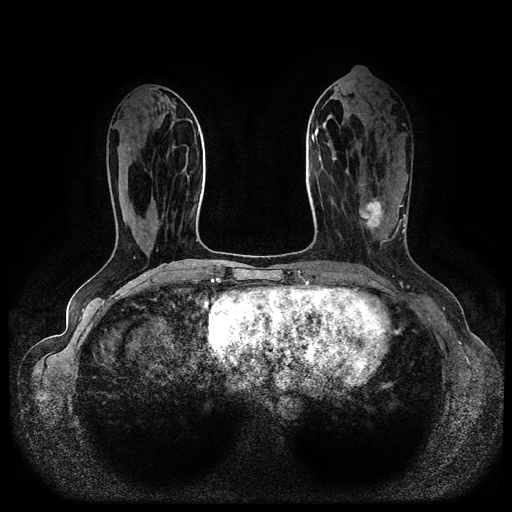
Breast MRI (dynamic contrast-enhanced, multi-phase), one axial slice; slice 38 of 116 in the series (ordered by position); dynamic contrast-enhanced series, time point 2 of 5 at this slice position (early post-contrast); 1.5 T; TE 2.6 ms, TR 5.3 ms; 2 mm slice thickness; 512 × 512 image matrix. Patient: female, 45 years.
Annotated regions visible in this slice (semi-automatically segmented with operator editing):
- breast lesion (labelled 'tumour' in the annotation; benign lesions carry a separate 'benign' label): bounding box <358,196,389,233> (left, top, right, bottom; pixels)